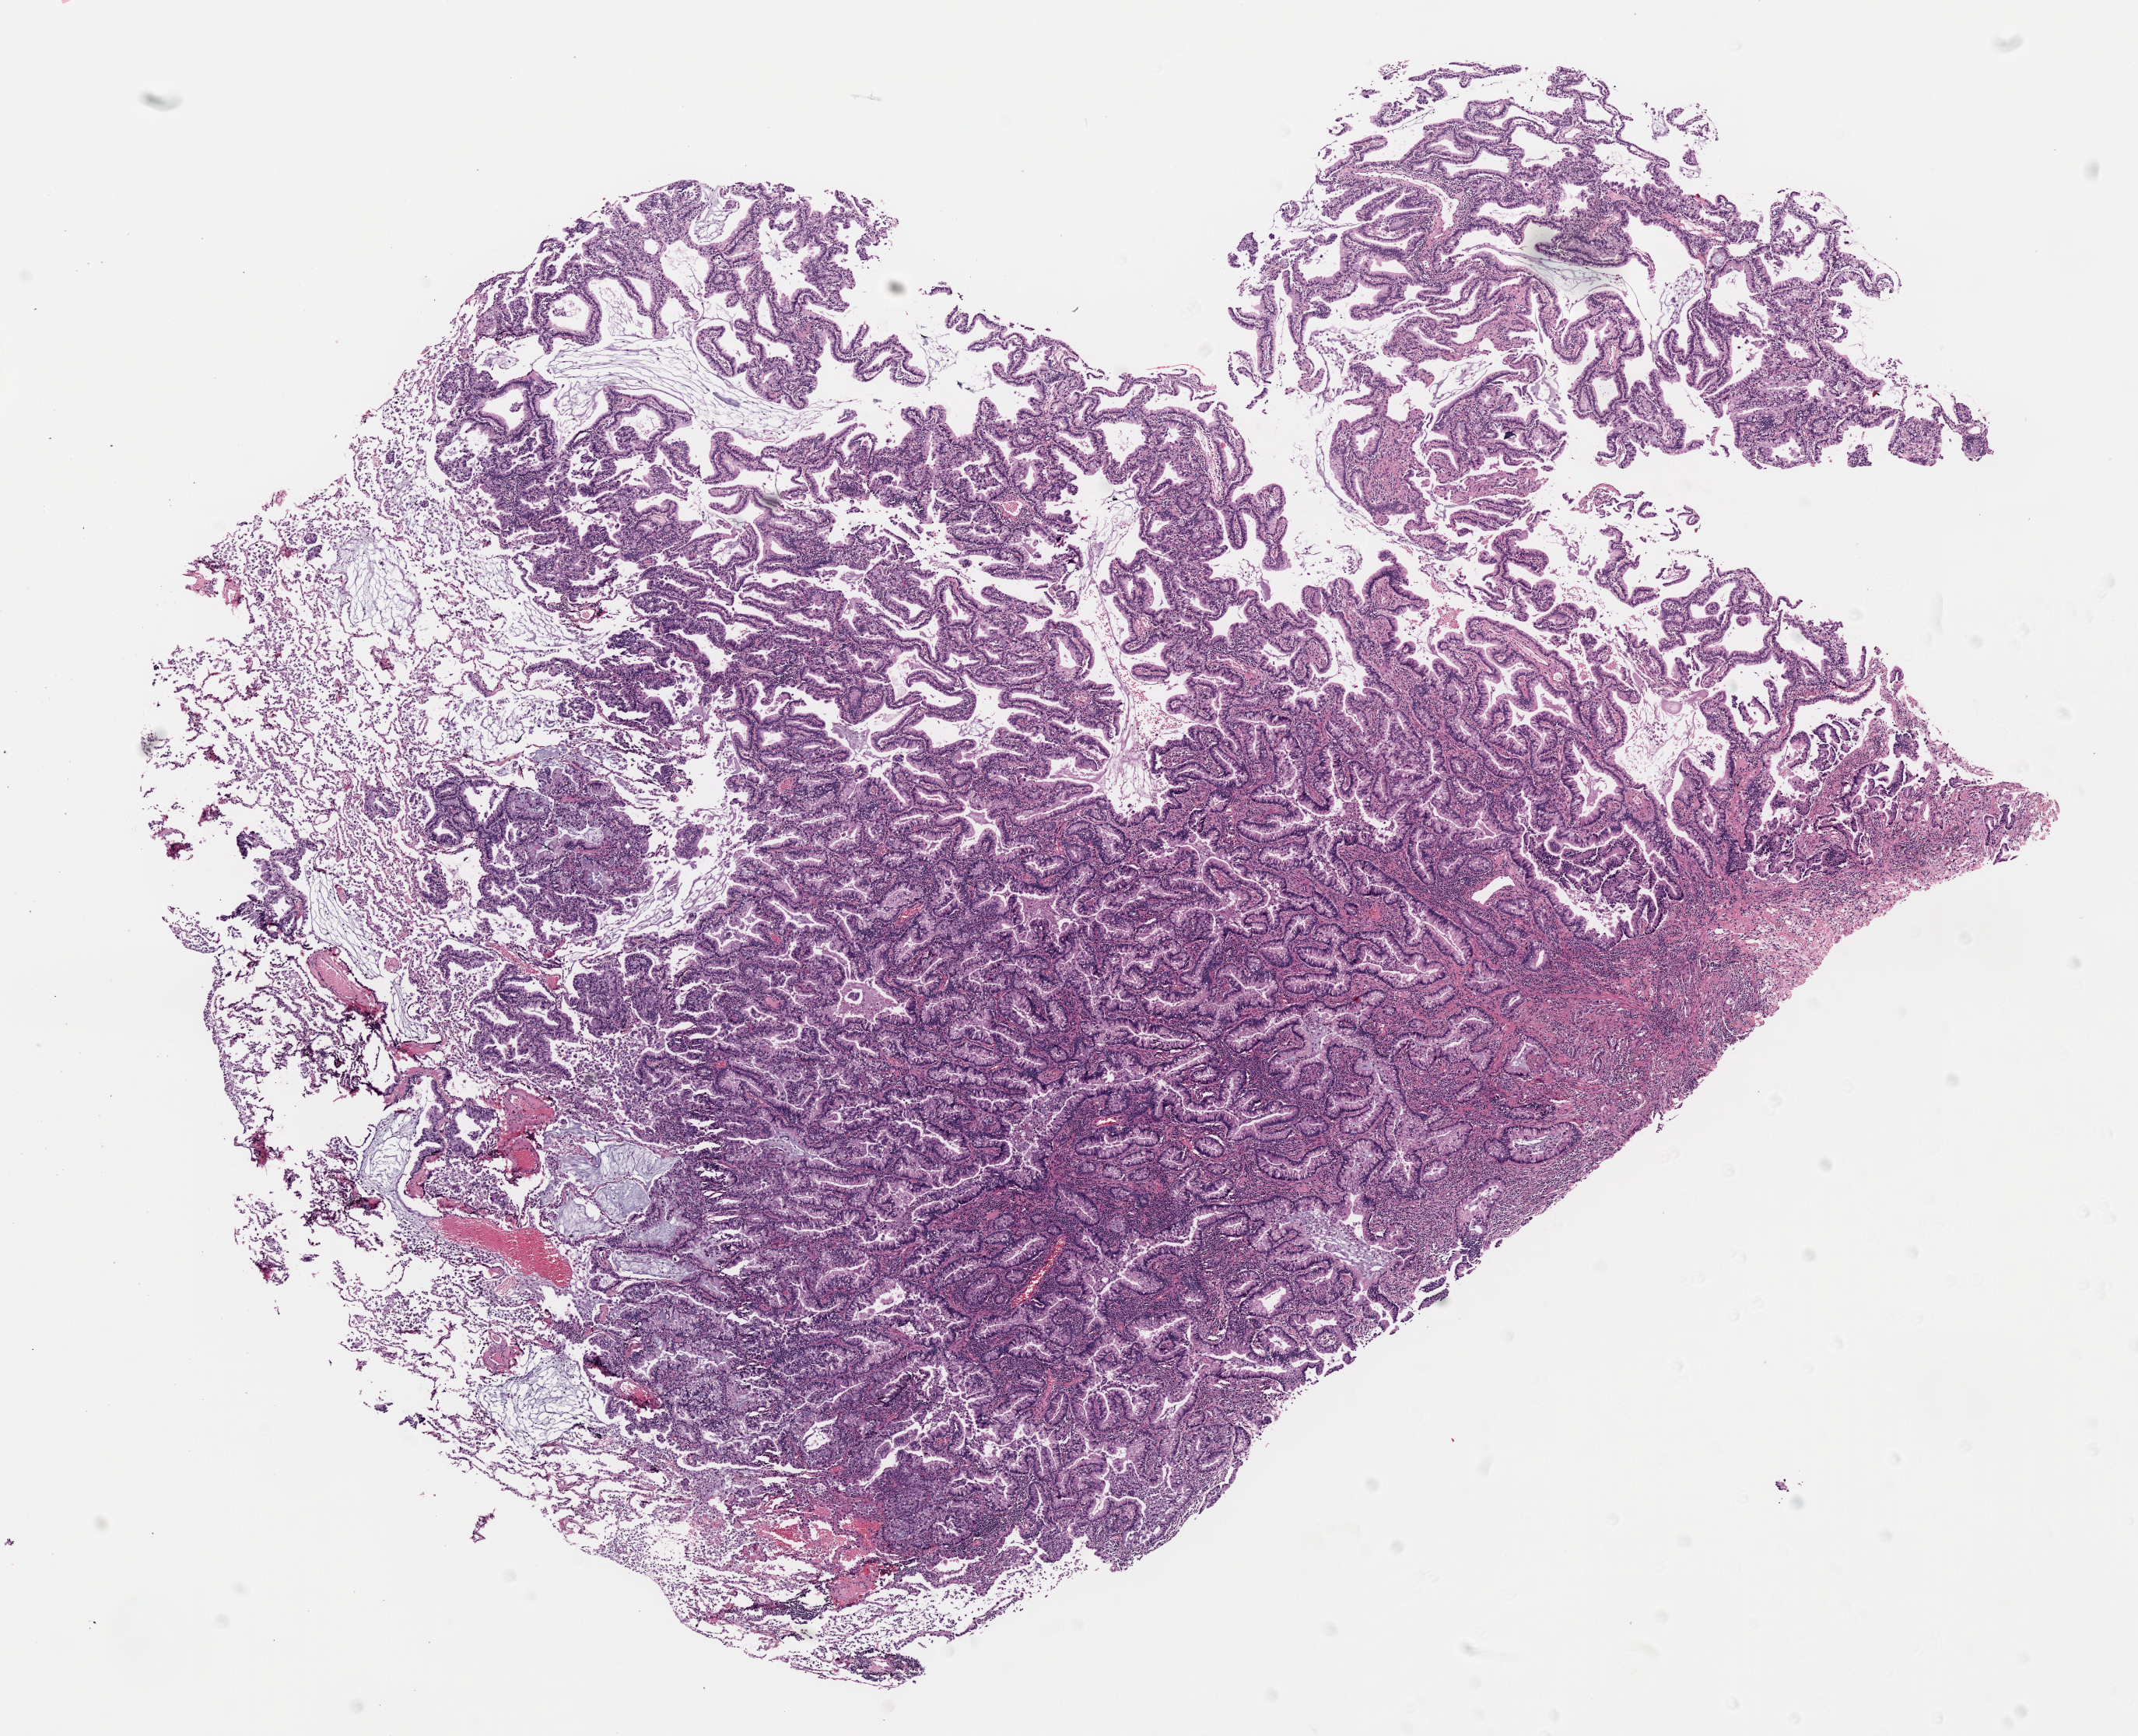
Hematoxylin and eosin (H&E) stained whole-slide image, whole scanned area (about 11.0 x 8.9 mm, acquisition: 20x scan) shown as a low-resolution overview; formalin-fixed paraffin-embedded (FFPE) diagnostic section; sample: primary tumour, lung. Female patient.
AJCC pathologic stage: IA (6th edition). Histologic diagnosis: Adenocarcinoma, NOS. Laterality: right.